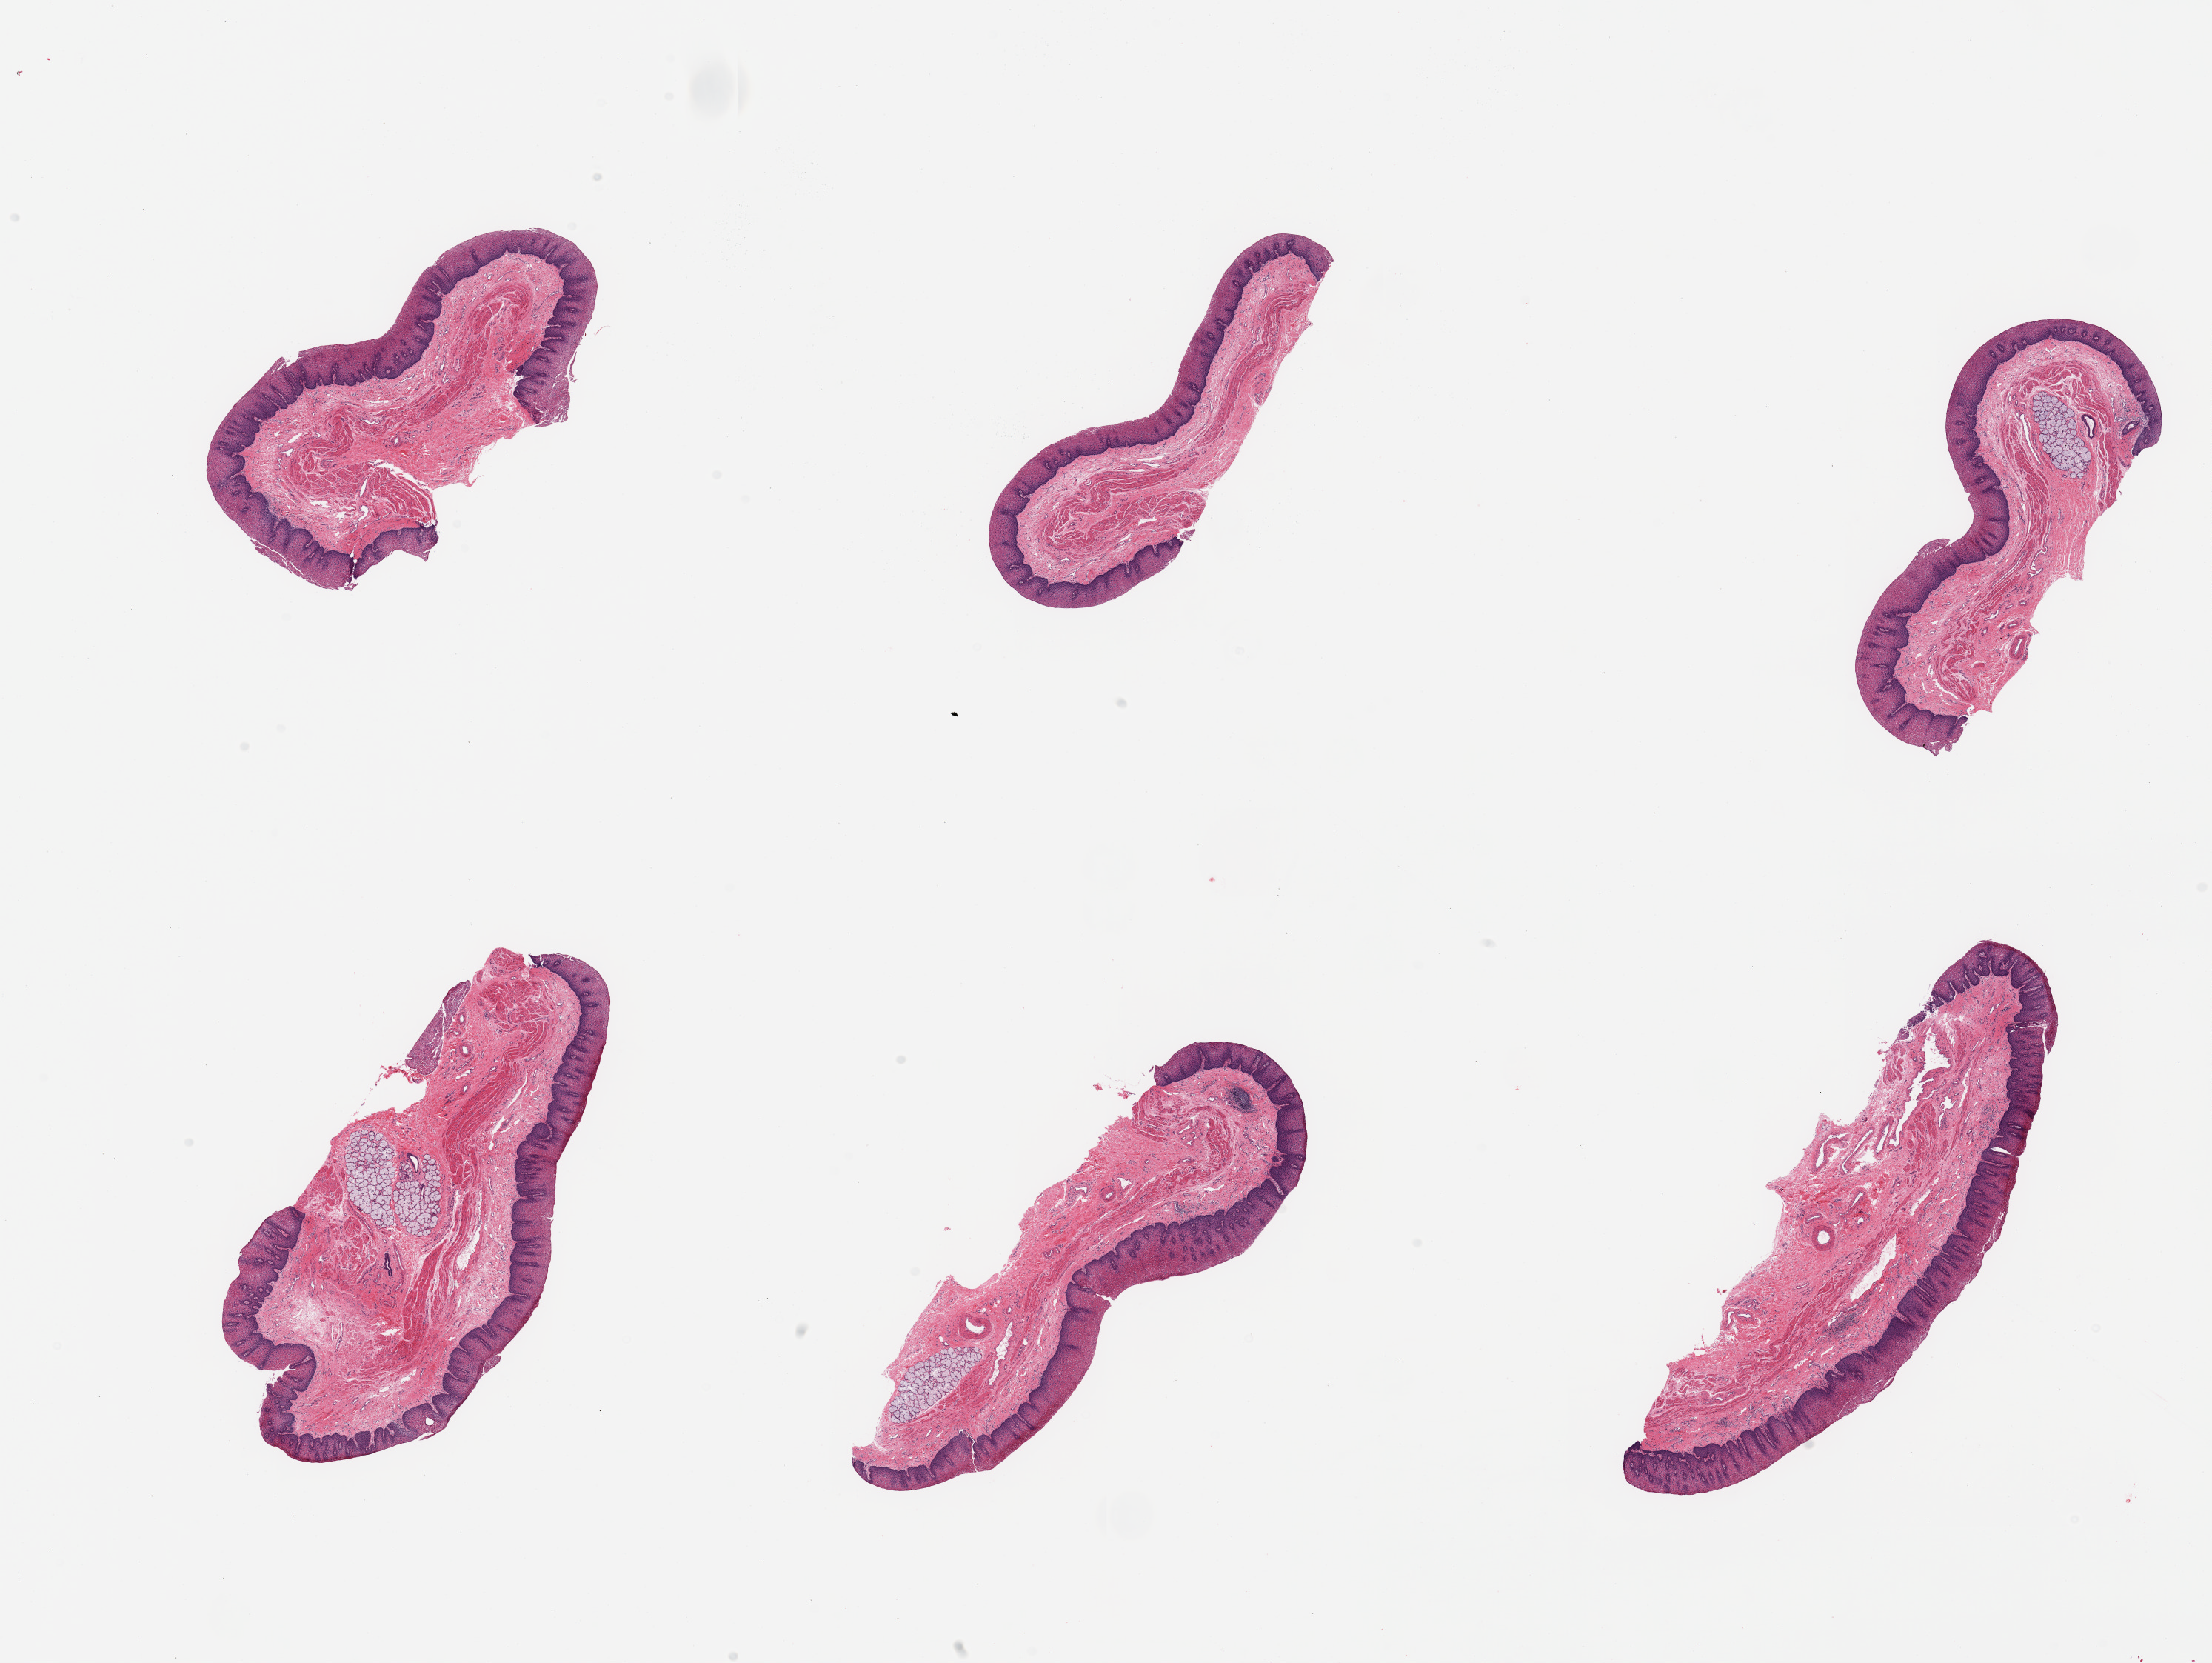
Haematoxylin and eosin whole-slide image, a low-resolution overview of the entire scanned area, about 23.6 x 17.8 mm; PAXgene-fixed, paraffin-embedded tissue; sampled site (target tissue): esophageal mucous membrane; tissue donor sample.
Reviewer comment on this tissue sample: 6 pieces, squamous mucosa up to ~0.5mm, ~30% thickness.